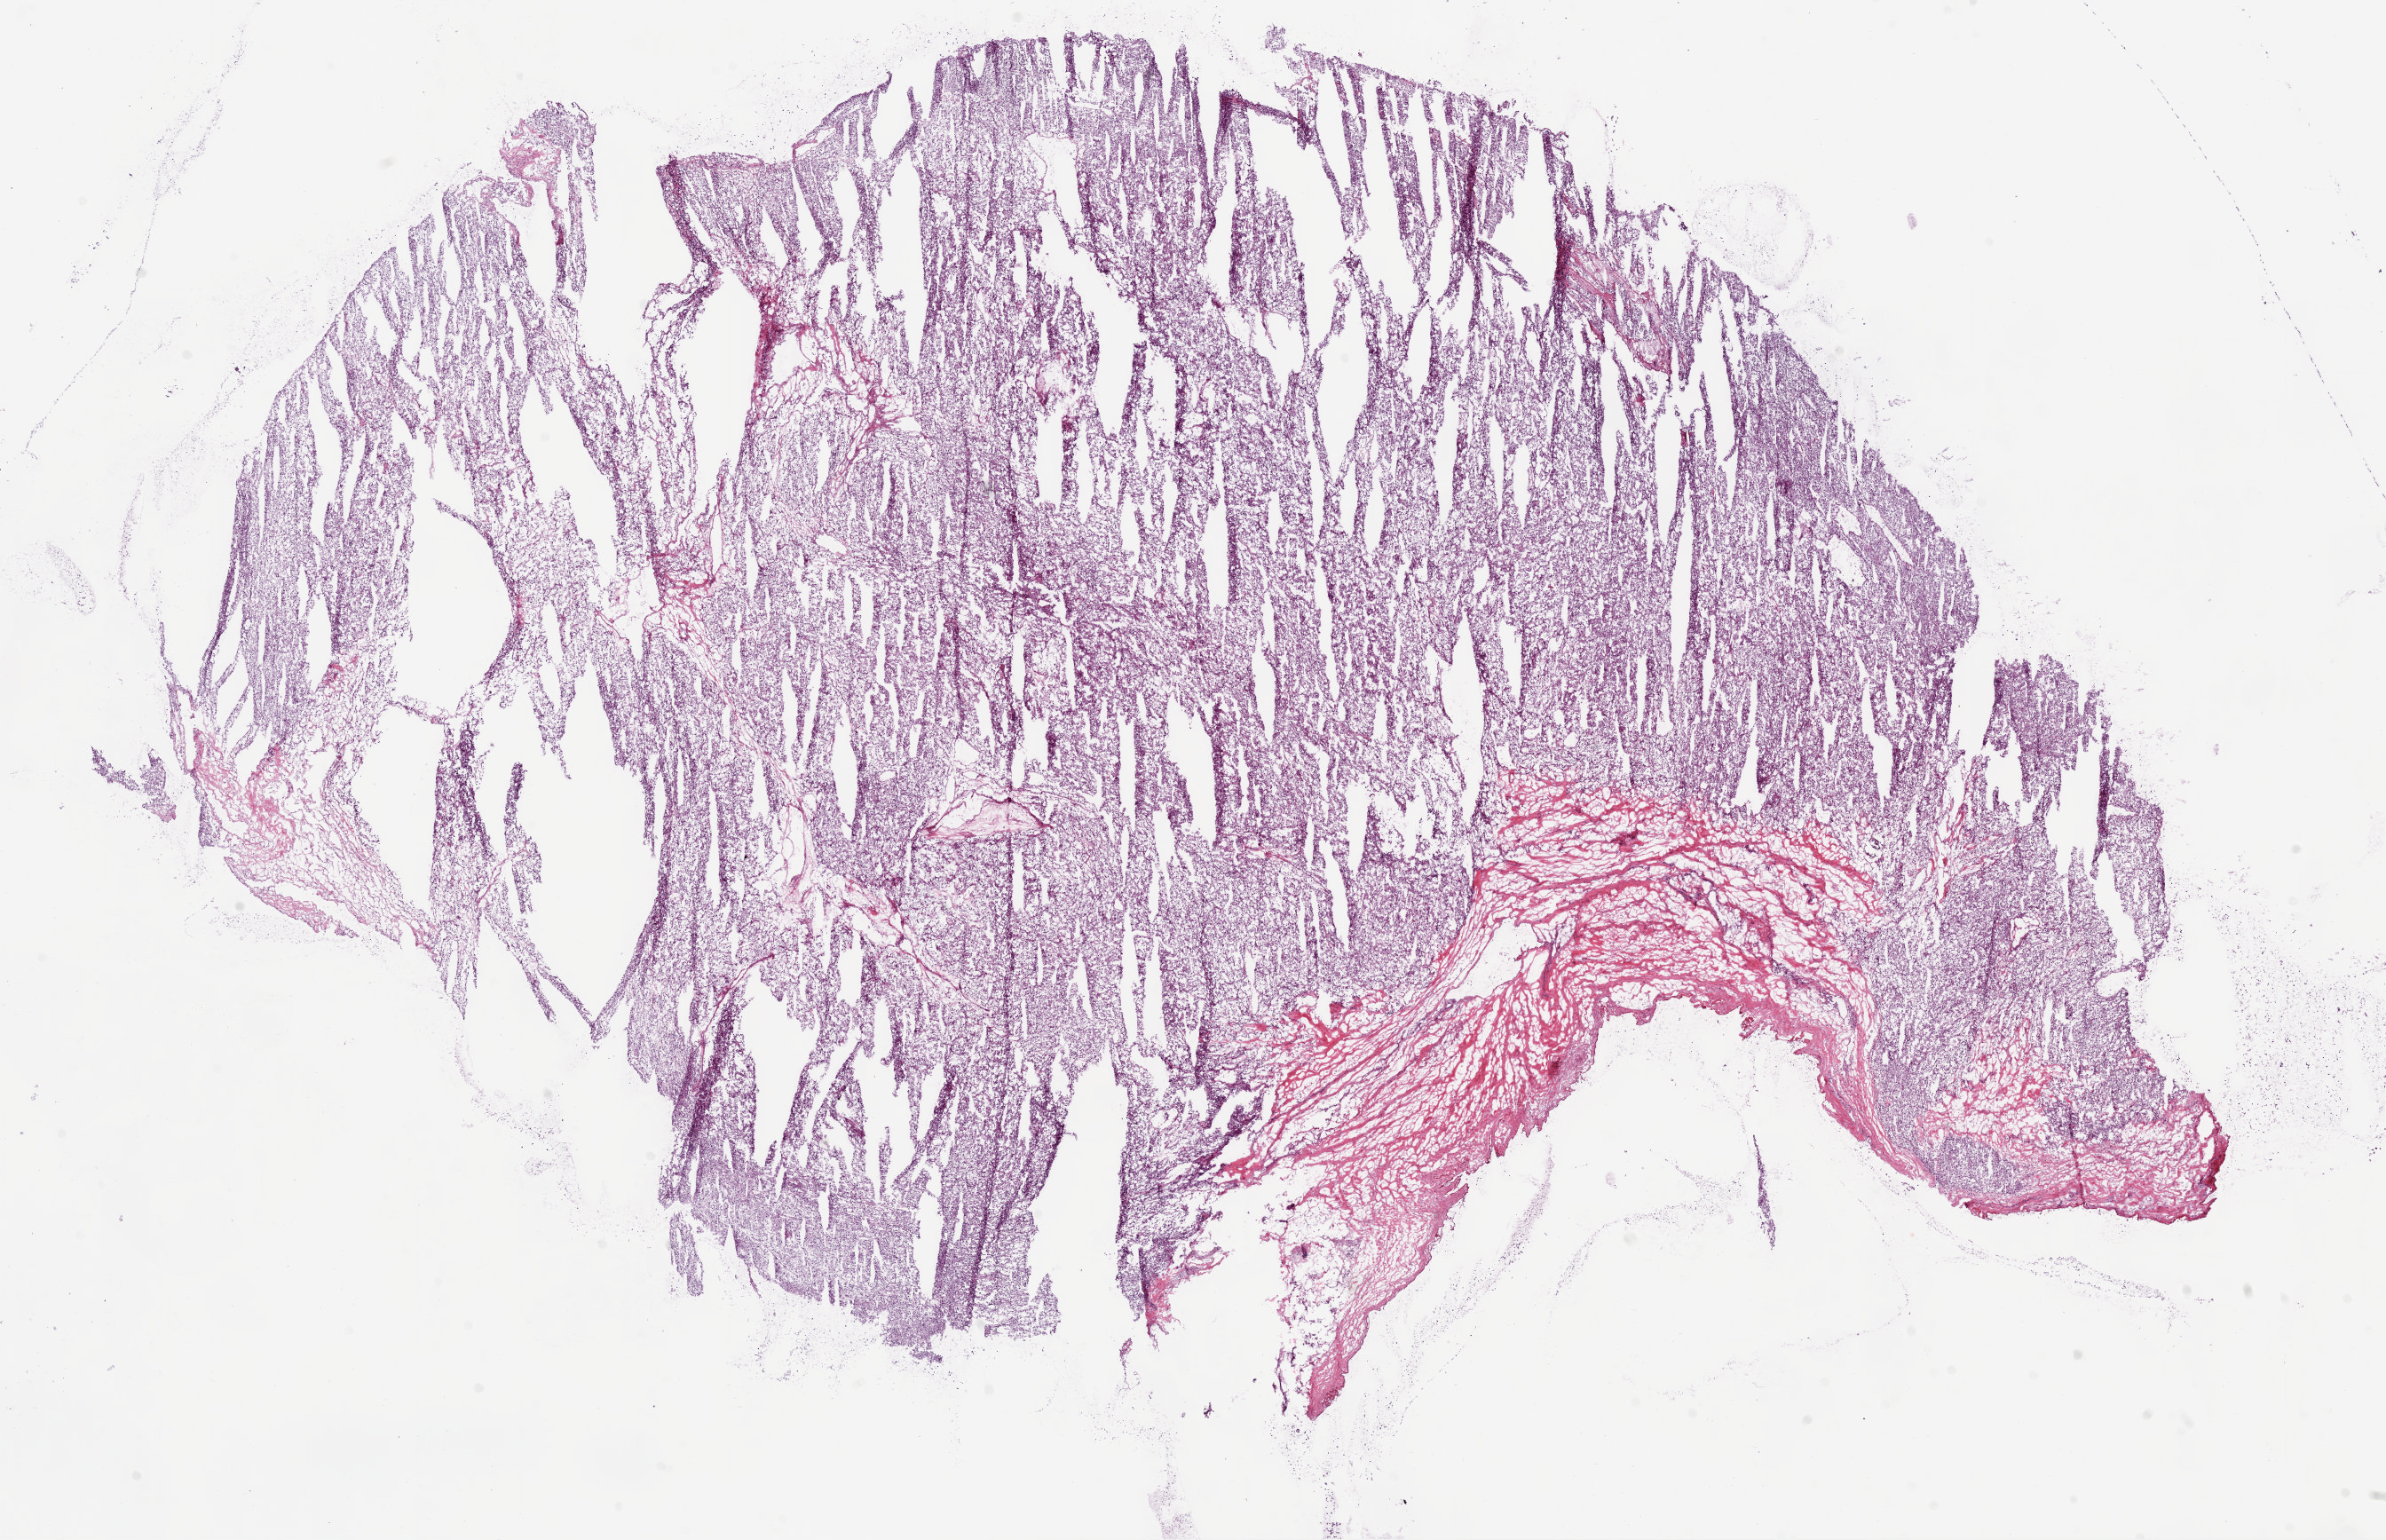
H&E-stained whole-slide image, a low-resolution overview of the entire scanned area, about 21.5 x 13.9 mm (acquisition: 5x scan), frozen section from the top of the tissue portion, sample: primary tumour, kidney. Male, age 64 years at initial diagnosis. Histologic grade: G4 (undifferentiated). Composition of this section per pathologist review: tumour cells 95%, tumour nuclei 85%, normal cells 0%, stromal cells 5%, necrosis 0%.
Laterality: left. Diagnosis: Clear cell adenocarcinoma, NOS. AJCC pathologic stage: IV.